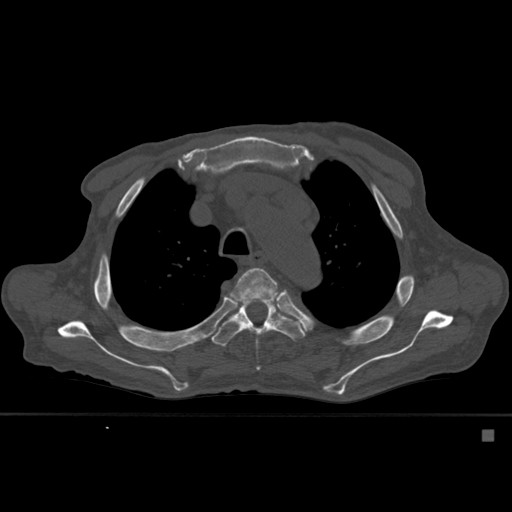
CT including the spine, one axial slice. Slice 408 of 527 in the series (ordered by position). Bone window (W 1800 / L 400 HU). 1.5 mm slice thickness. 512 × 512 image matrix, field of view 373 × 373 mm. Male patient, age 78 years. From the clinical record (not read from this slice): primary cancer: prostate.
Structures marked on this image (semi-automatic segmentation, software-assisted and operator-edited):
- T4 vertebra: box from (x=230, y=268) to (x=280, y=371) px
- T5 vertebra: (x=211, y=298)–(x=306, y=347)